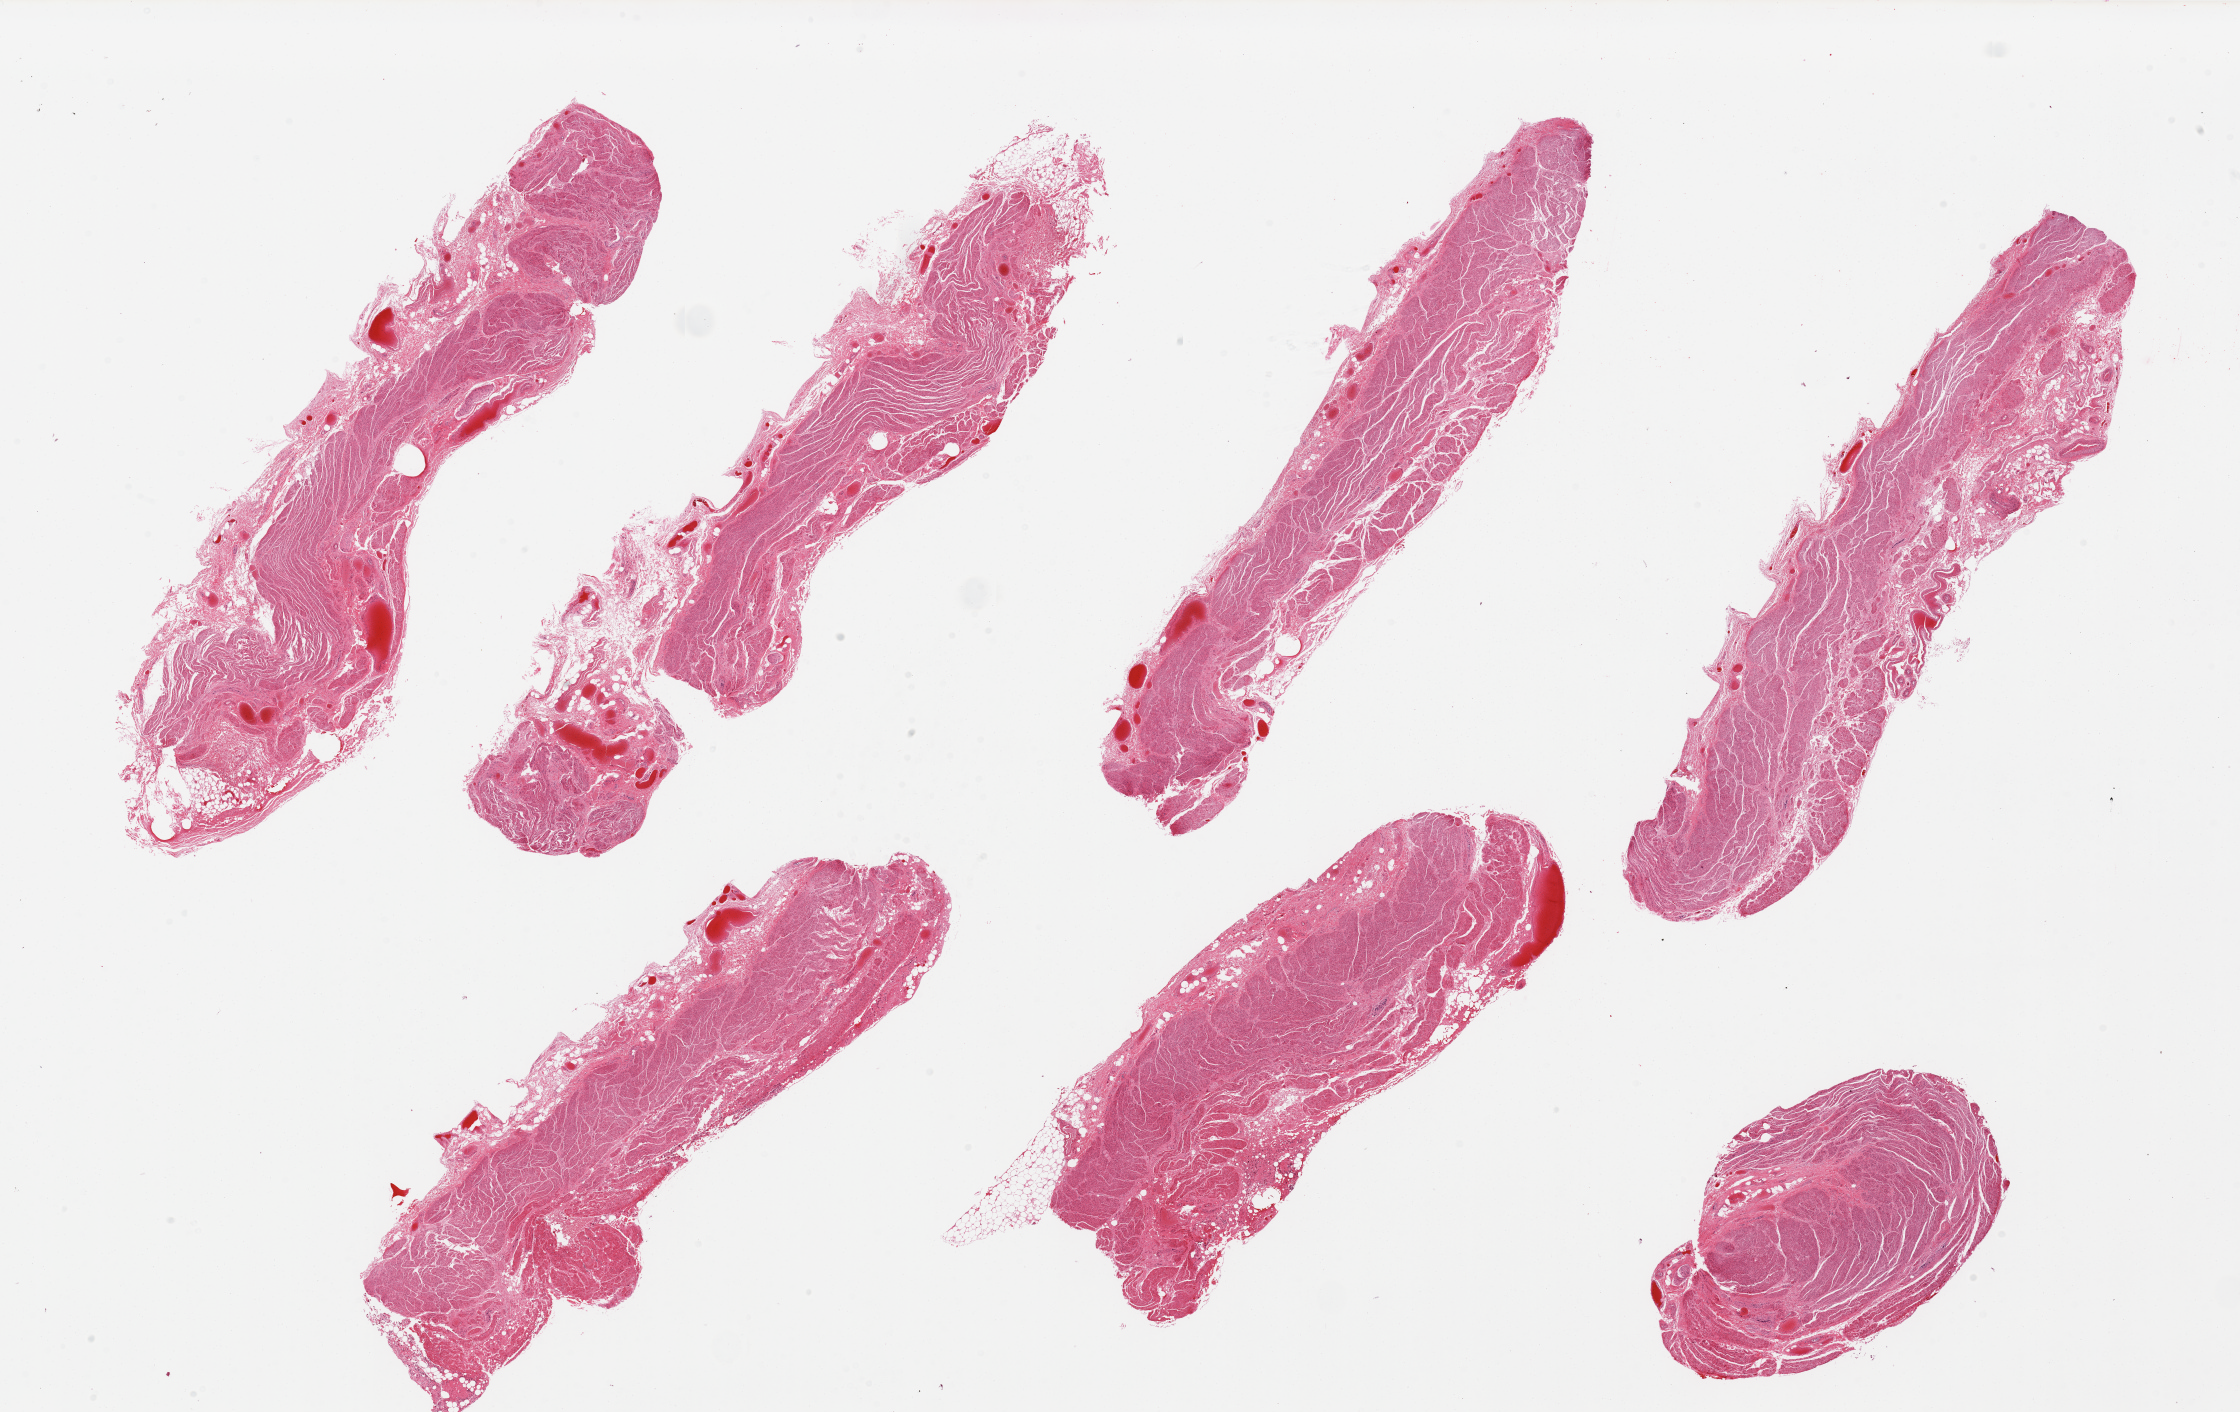
Digitized hematoxylin and eosin (H&E)-stained section, shown as a low-resolution overview of the whole scanned area (about 35.4 x 22.3 mm). PAXgene-fixed paraffin-embedded (PFPE) section. Target tissue: gastroesophageal junction. Donor tissue sample. Donor: male.
Review note (as recorded): 7 pieces, well trimmed of mucosa.